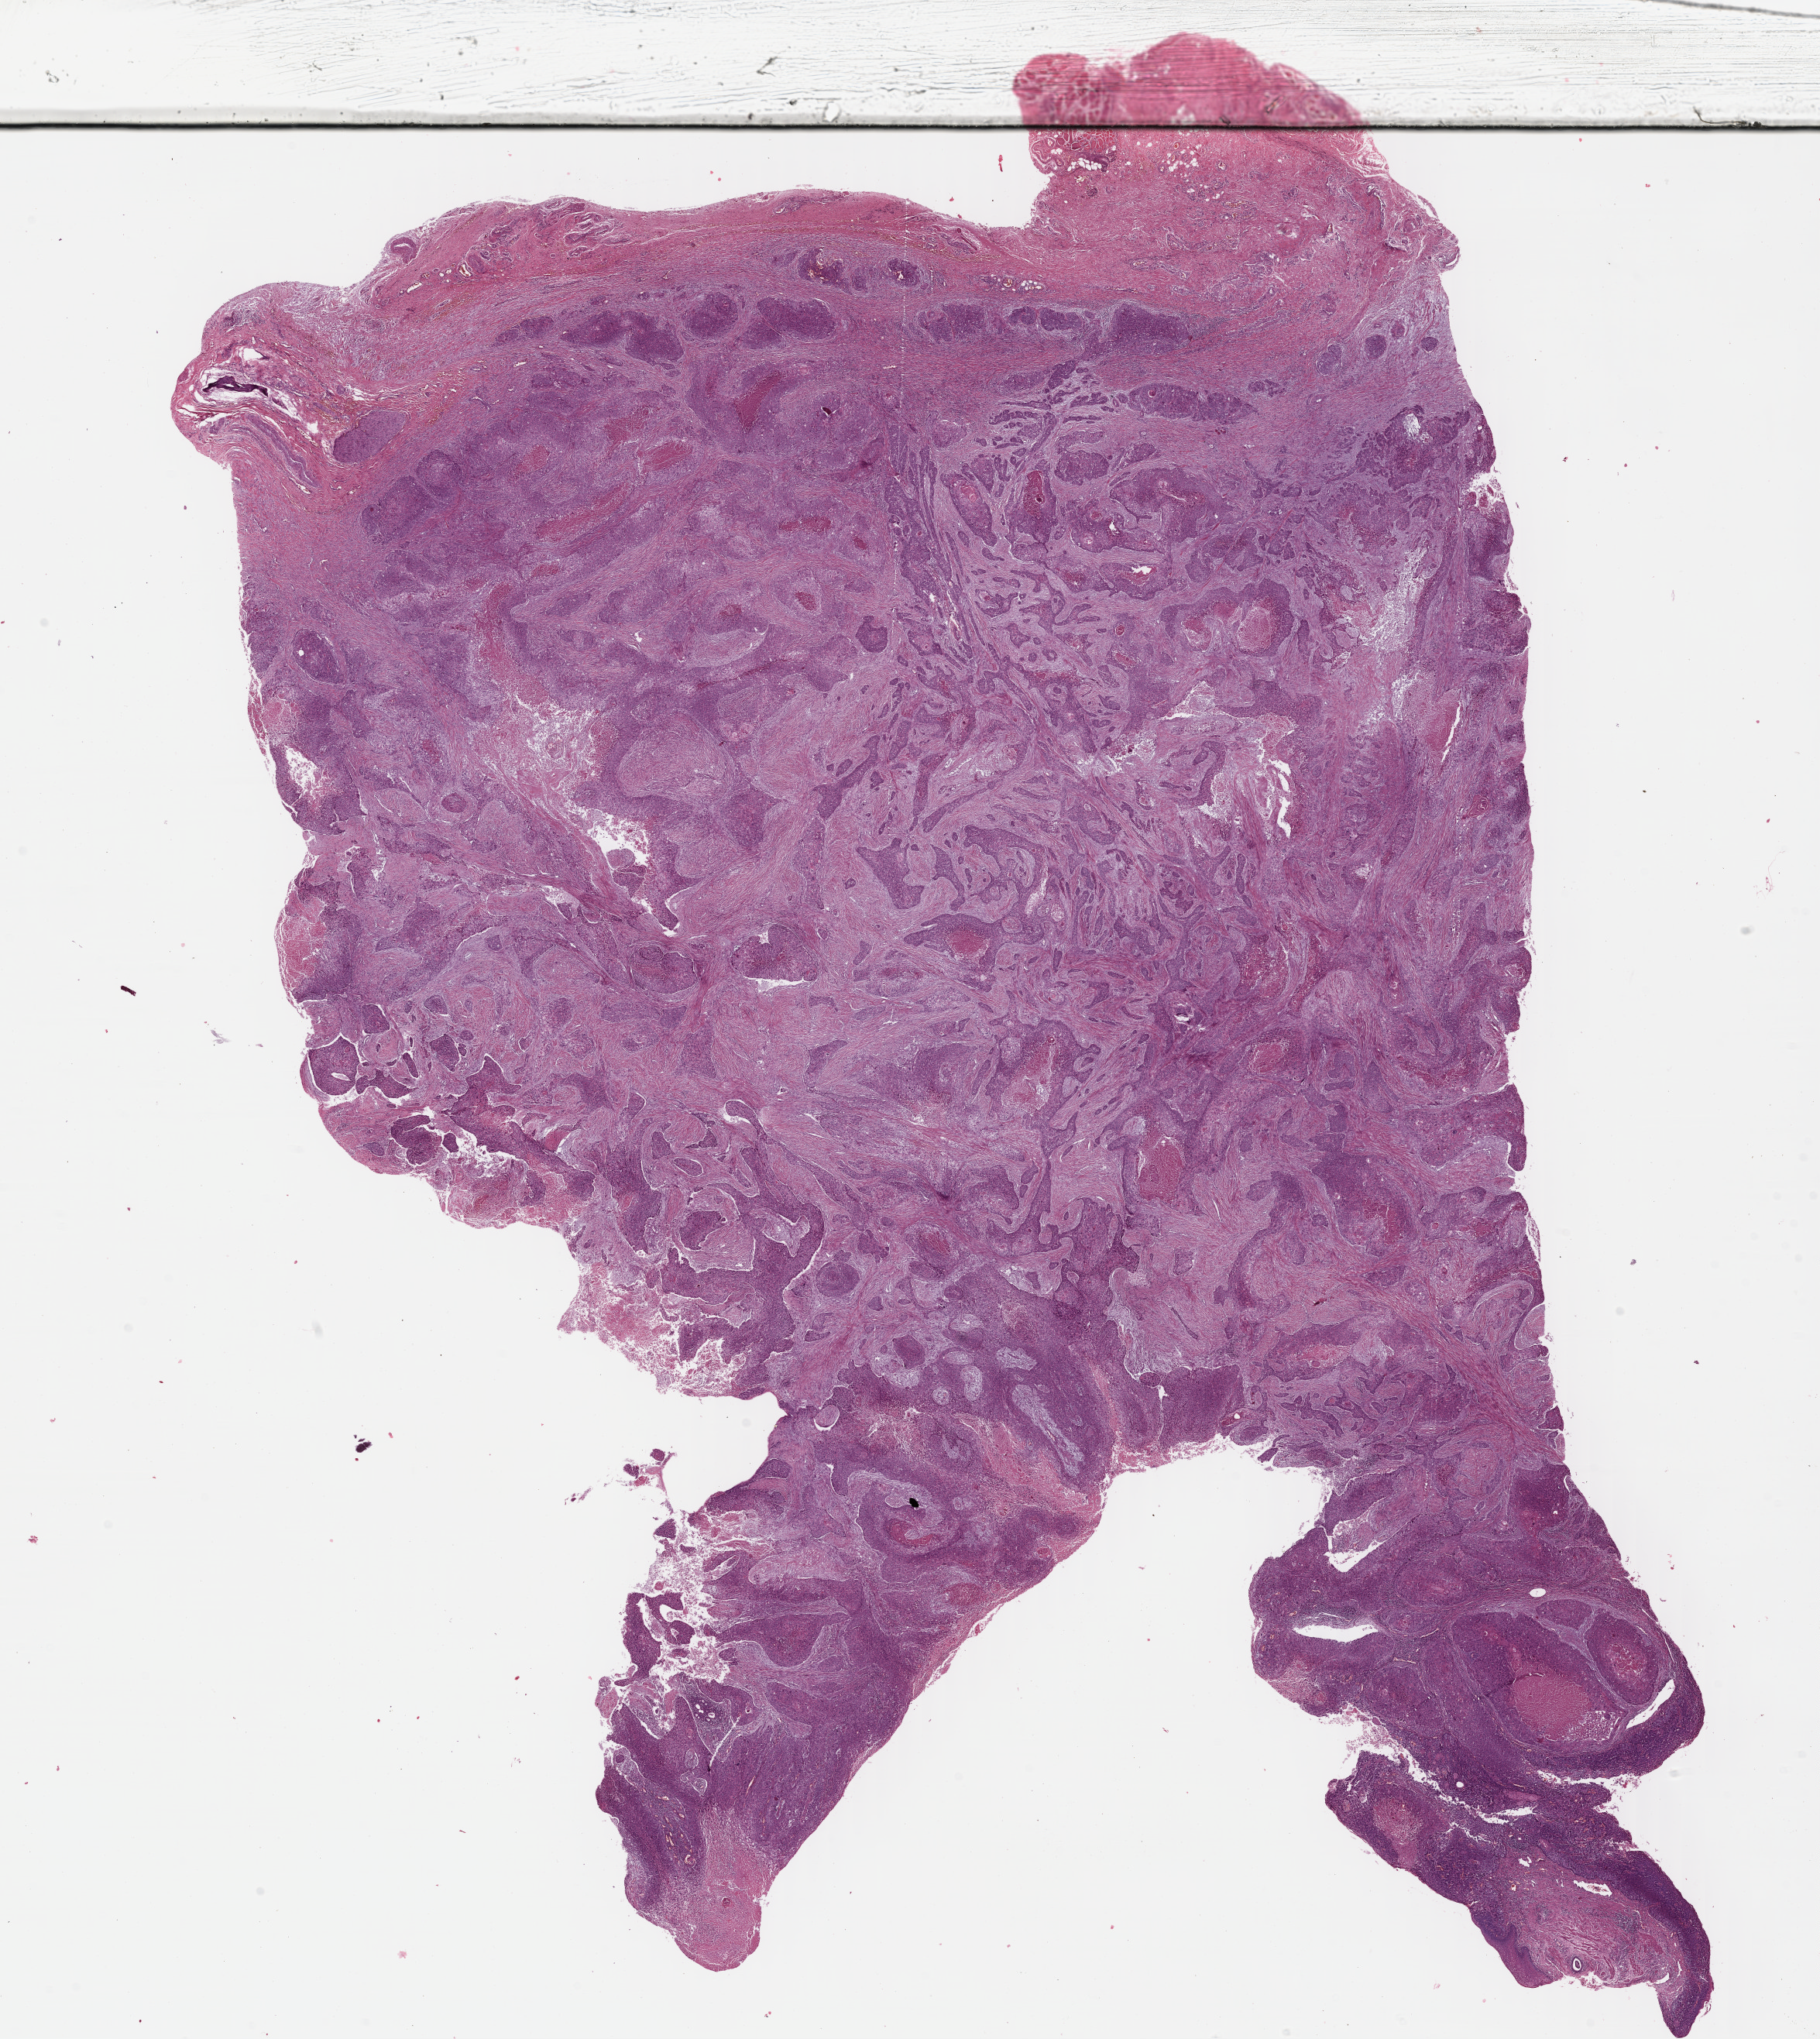
Hematoxylin and eosin (H&E) stained whole-slide image, low-resolution overview of the scanned area, about 18.5 x 20.7 mm (acquisition: 40x scan). Formalin-fixed paraffin-embedded (FFPE) diagnostic section. Sample: primary tumour, esophagus. Male patient; age at initial diagnosis 54 years. Histologic grade: G2 (moderately differentiated).
Pathologic diagnosis: Squamous cell carcinoma, NOS (lower third of esophagus). Lymph nodes positive (case pathology): 1 of 2 examined. AJCC pathologic stage: IIB.